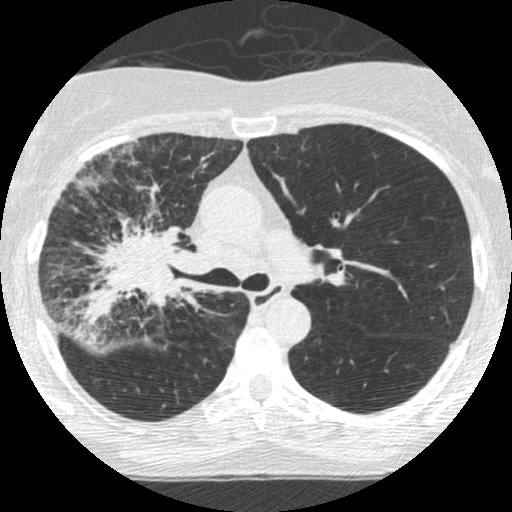
Low-dose screening chest CT, one axial slice. Position 169 of 253 along the scan axis. Reconstruction kernel STANDARD. Lung window (W 1500 / L -600 HU). 1.25 mm slice thickness. 512 × 512 image matrix, field of view 294 × 294 mm.
Outlined on this slice (manually delineated by an expert):
- lesion 2 (tumor, hilum of right lung): bounding box (x1, y1, x2, y2) in pixels: (74, 209, 187, 327)